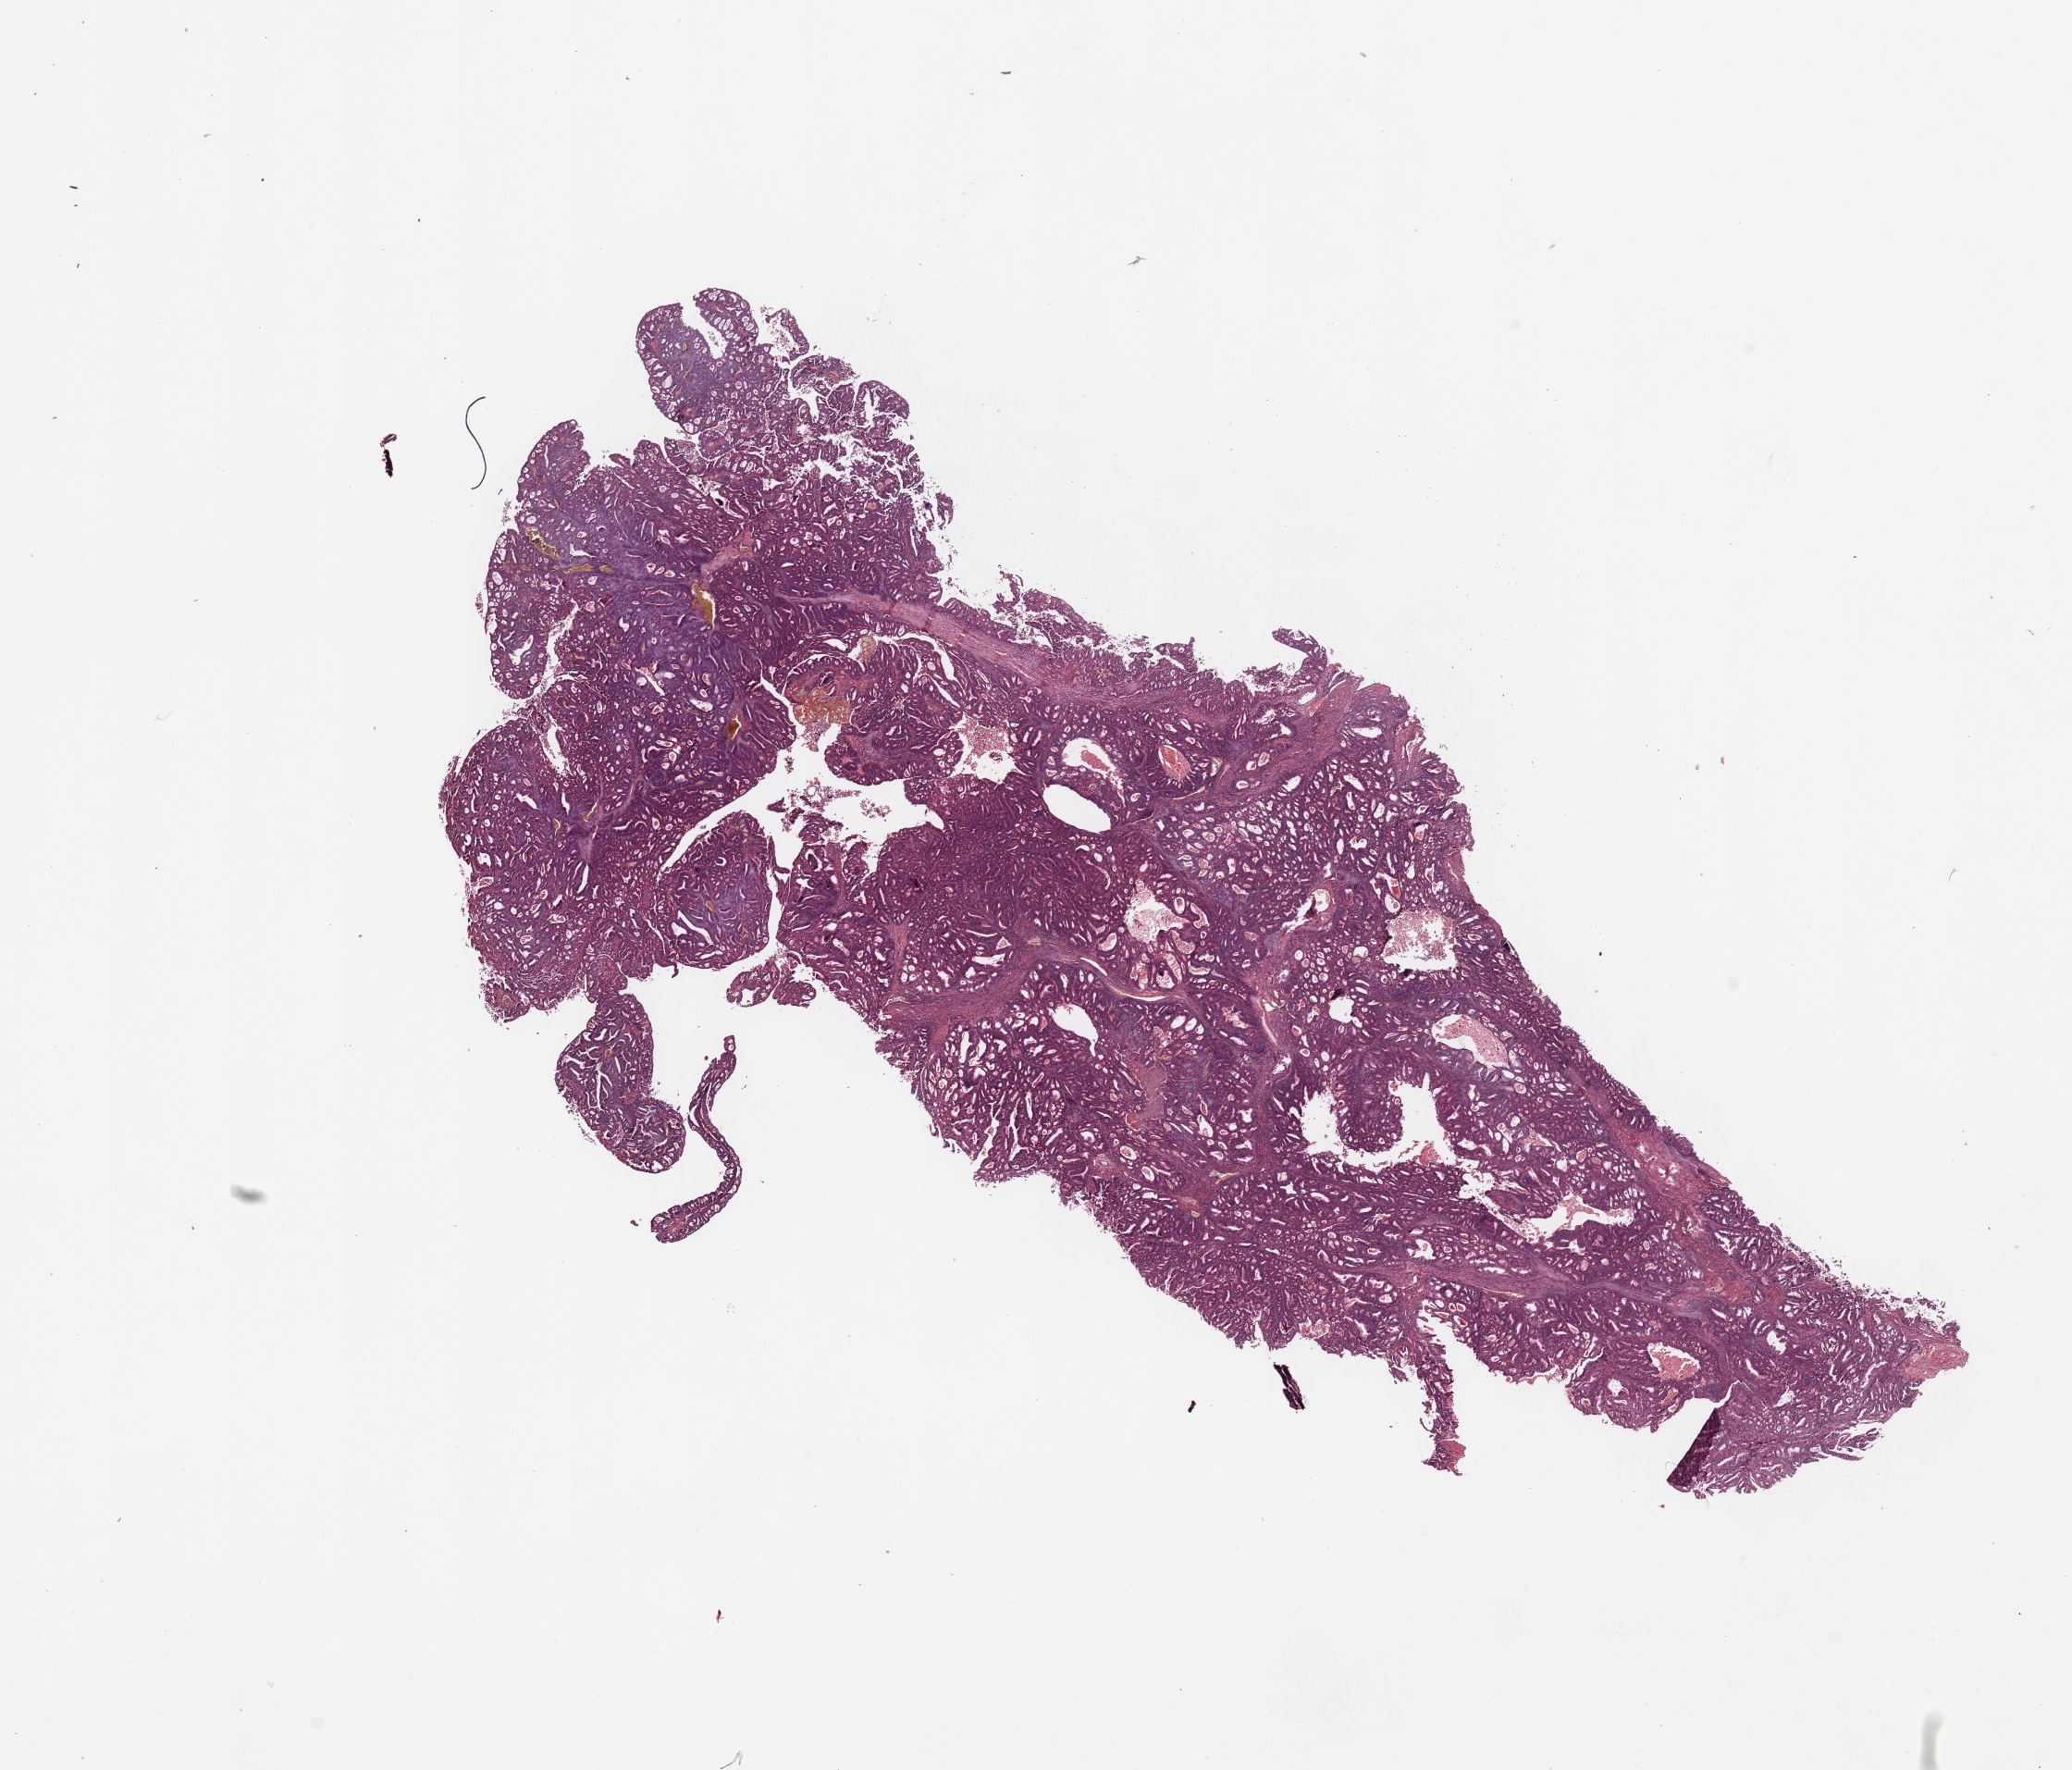
Whole-slide histology image, H&E, low-resolution overview of the scanned area, about 17.7 x 15.1 mm, tumour tissue sample, uterus. Female, 73 y/o. Histologic grade: G2 (moderately differentiated).
- histologic diagnosis: Endometrioid adenocarcinoma, NOS
- AJCC pathologic stage: I